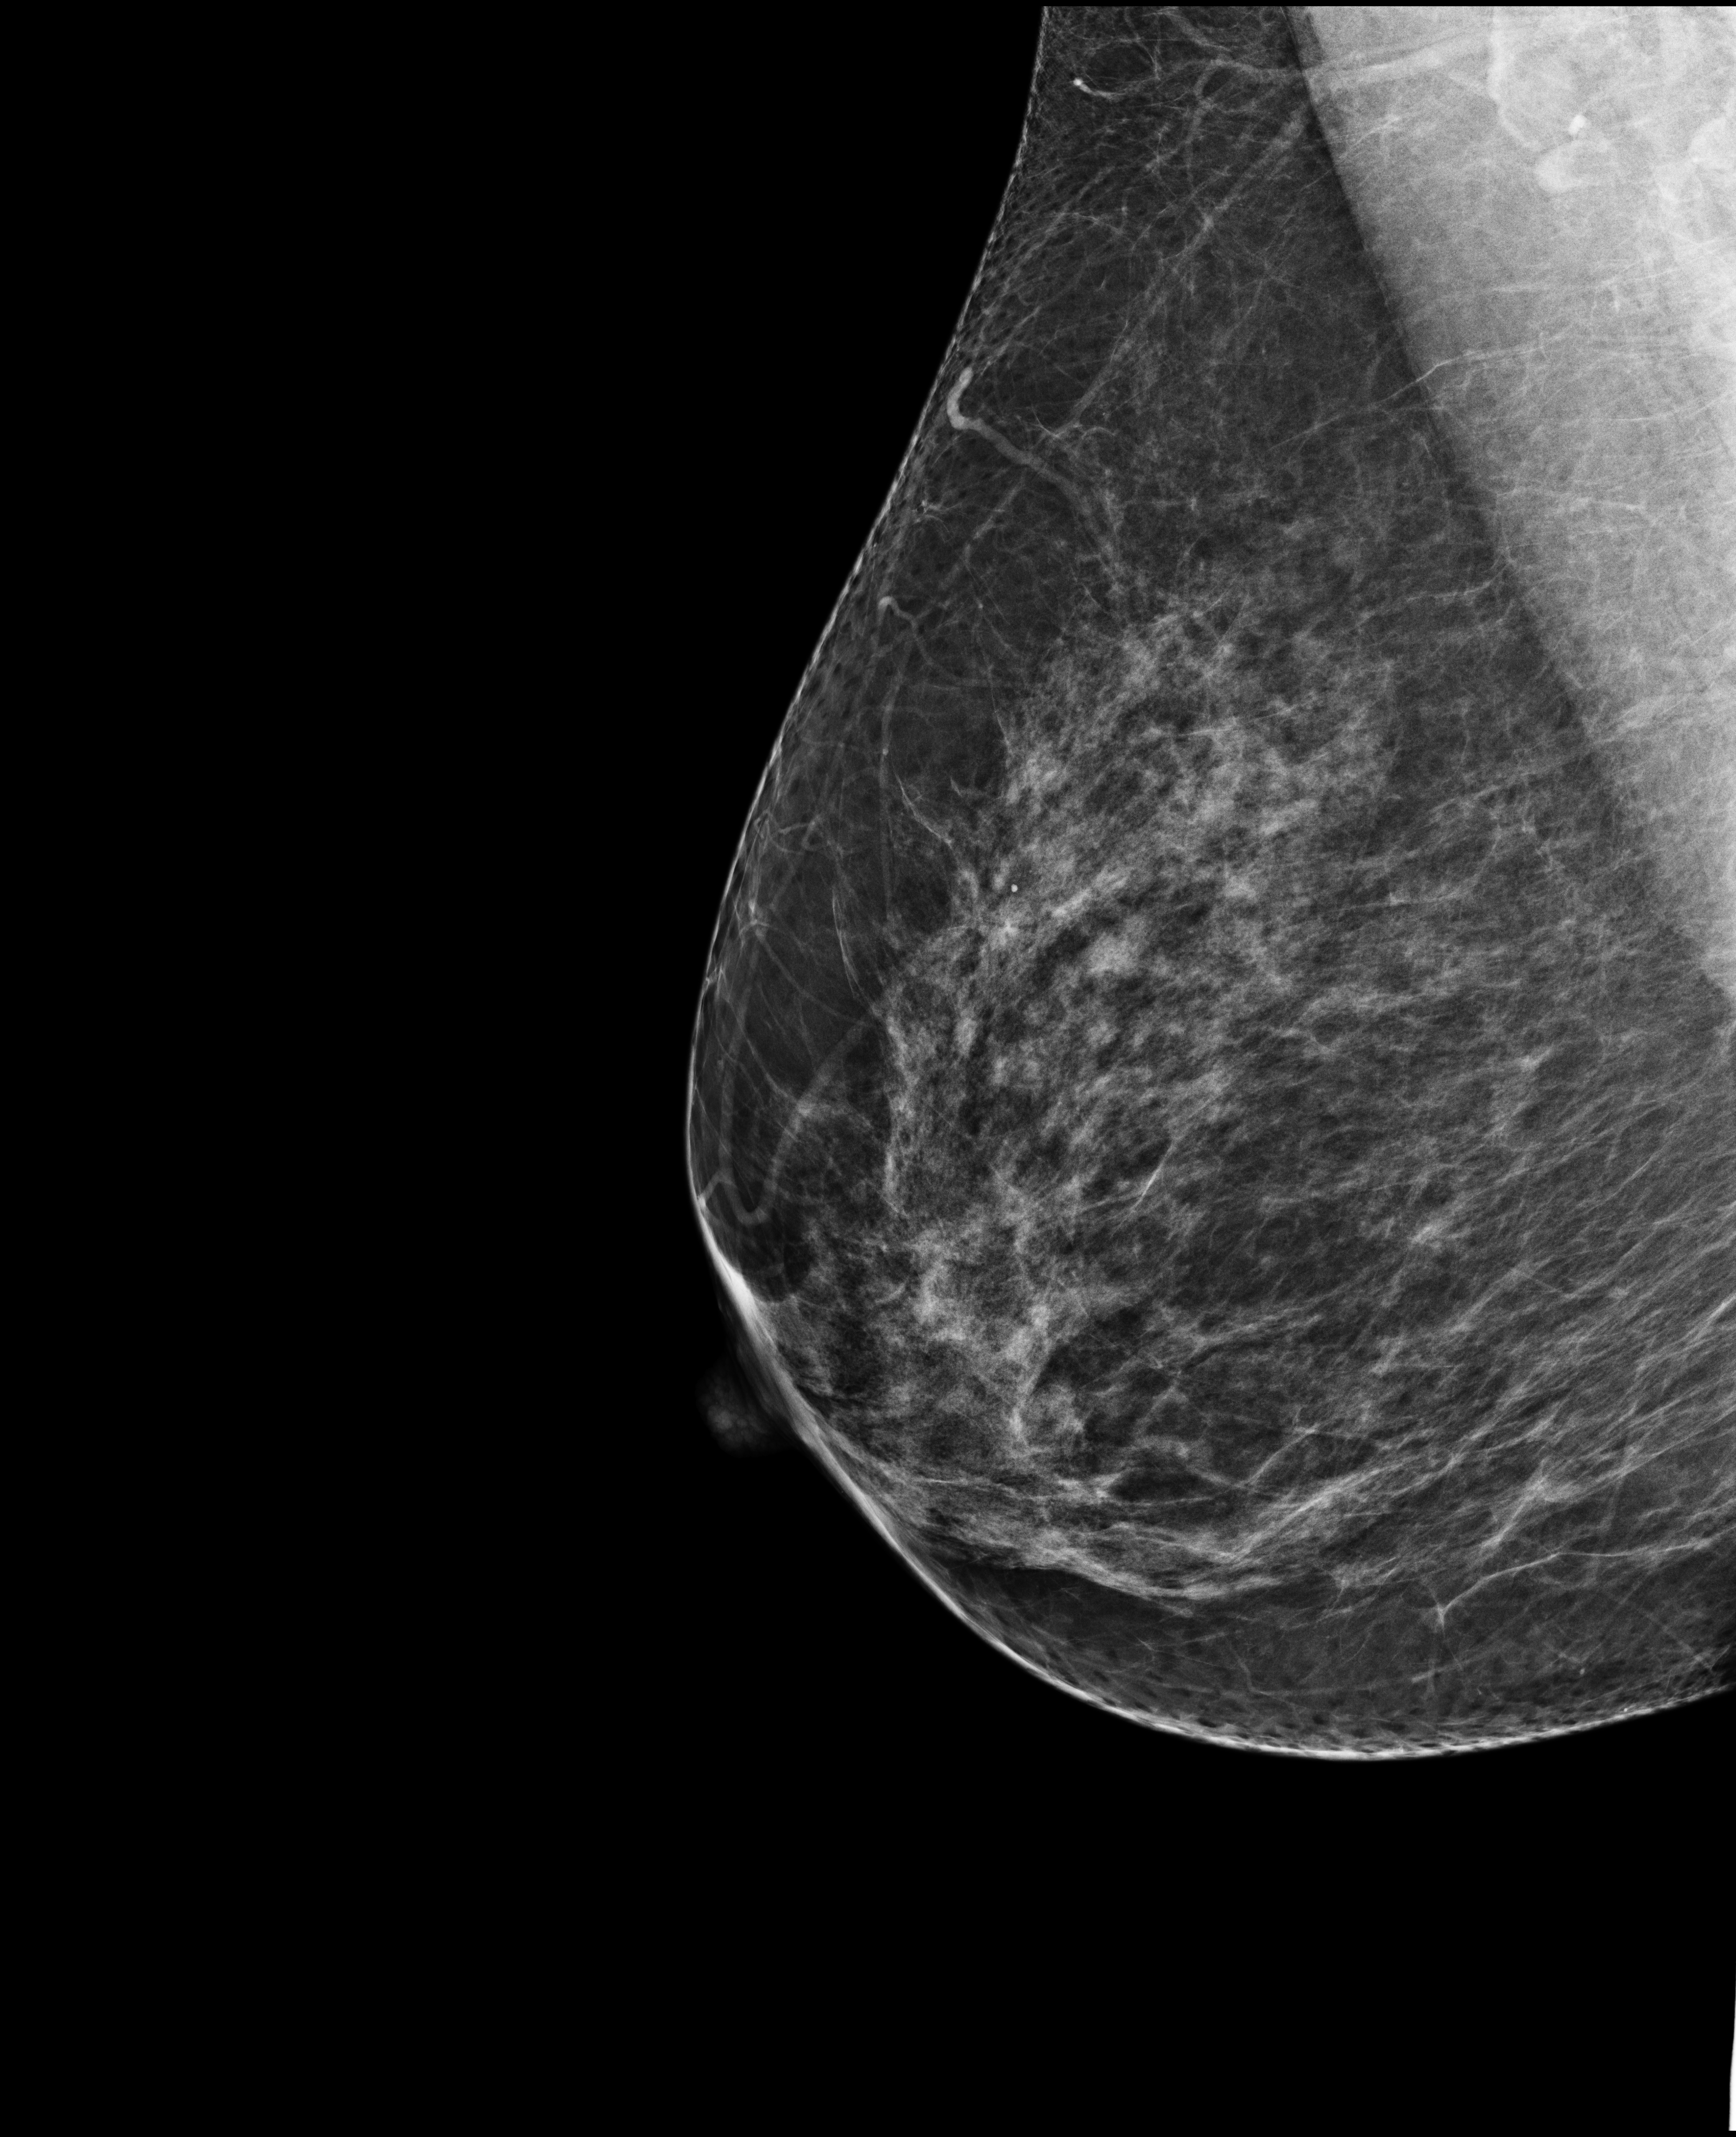
Annual screening mammography examination, compressed breast thickness 69 mm. Patient aged 48 years (female).
Image type: full-field digital mammogram. Breast: right. Projection: MLO view.